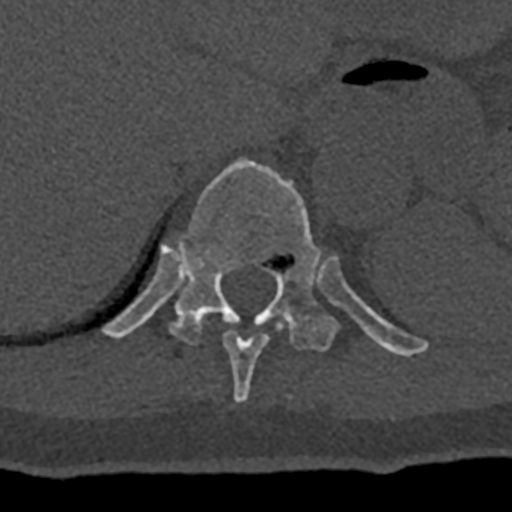
CT including the spine, one axial slice; slice 566 of 797 in the series (ordered by position); 120 kVp; bone window (W 1800 / L 400 HU); 512 × 512 image matrix. Patient: male, 74 years. Case-level facts recorded for this patient, not image findings: primary cancer: renal; vertebrae with lytic lesions (as recorded): T10, L1, L2, L3, L4, L5.
Structures marked on this image (semi-automatically segmented with operator editing):
- T10 vertebra: bounding box (x1, y1, x2, y2) in pixels: (223, 330, 269, 404)
- T11 vertebra: (102, 158, 428, 357)